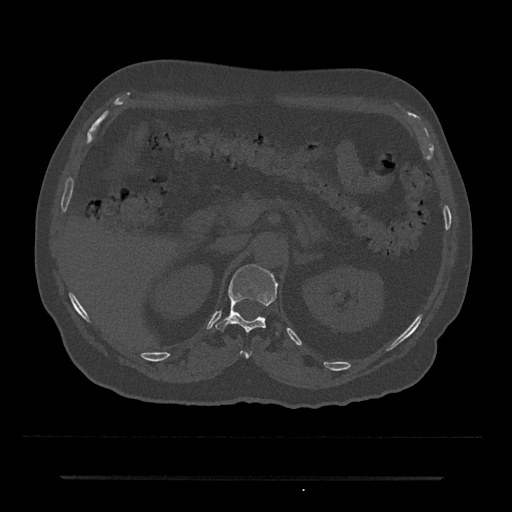
CT including the spine, one axial slice. Slice 127 of 797 in the series (ordered by position). Reconstruction kernel Br40s/3. Bone window (W 1800 / L 400 HU). 0.5 mm slice thickness. 512 × 512 image matrix, field of view 437 × 437 mm. Male patient, age 69 years. Case-level facts recorded for this patient, not image findings: primary cancer: prostate.
Structures marked on this image (semi-automatically segmented with operator editing):
- T11 vertebra: bounding box (x1, y1, x2, y2) in pixels: (240, 351, 251, 358)
- T12 vertebra: (215, 264, 279, 336)